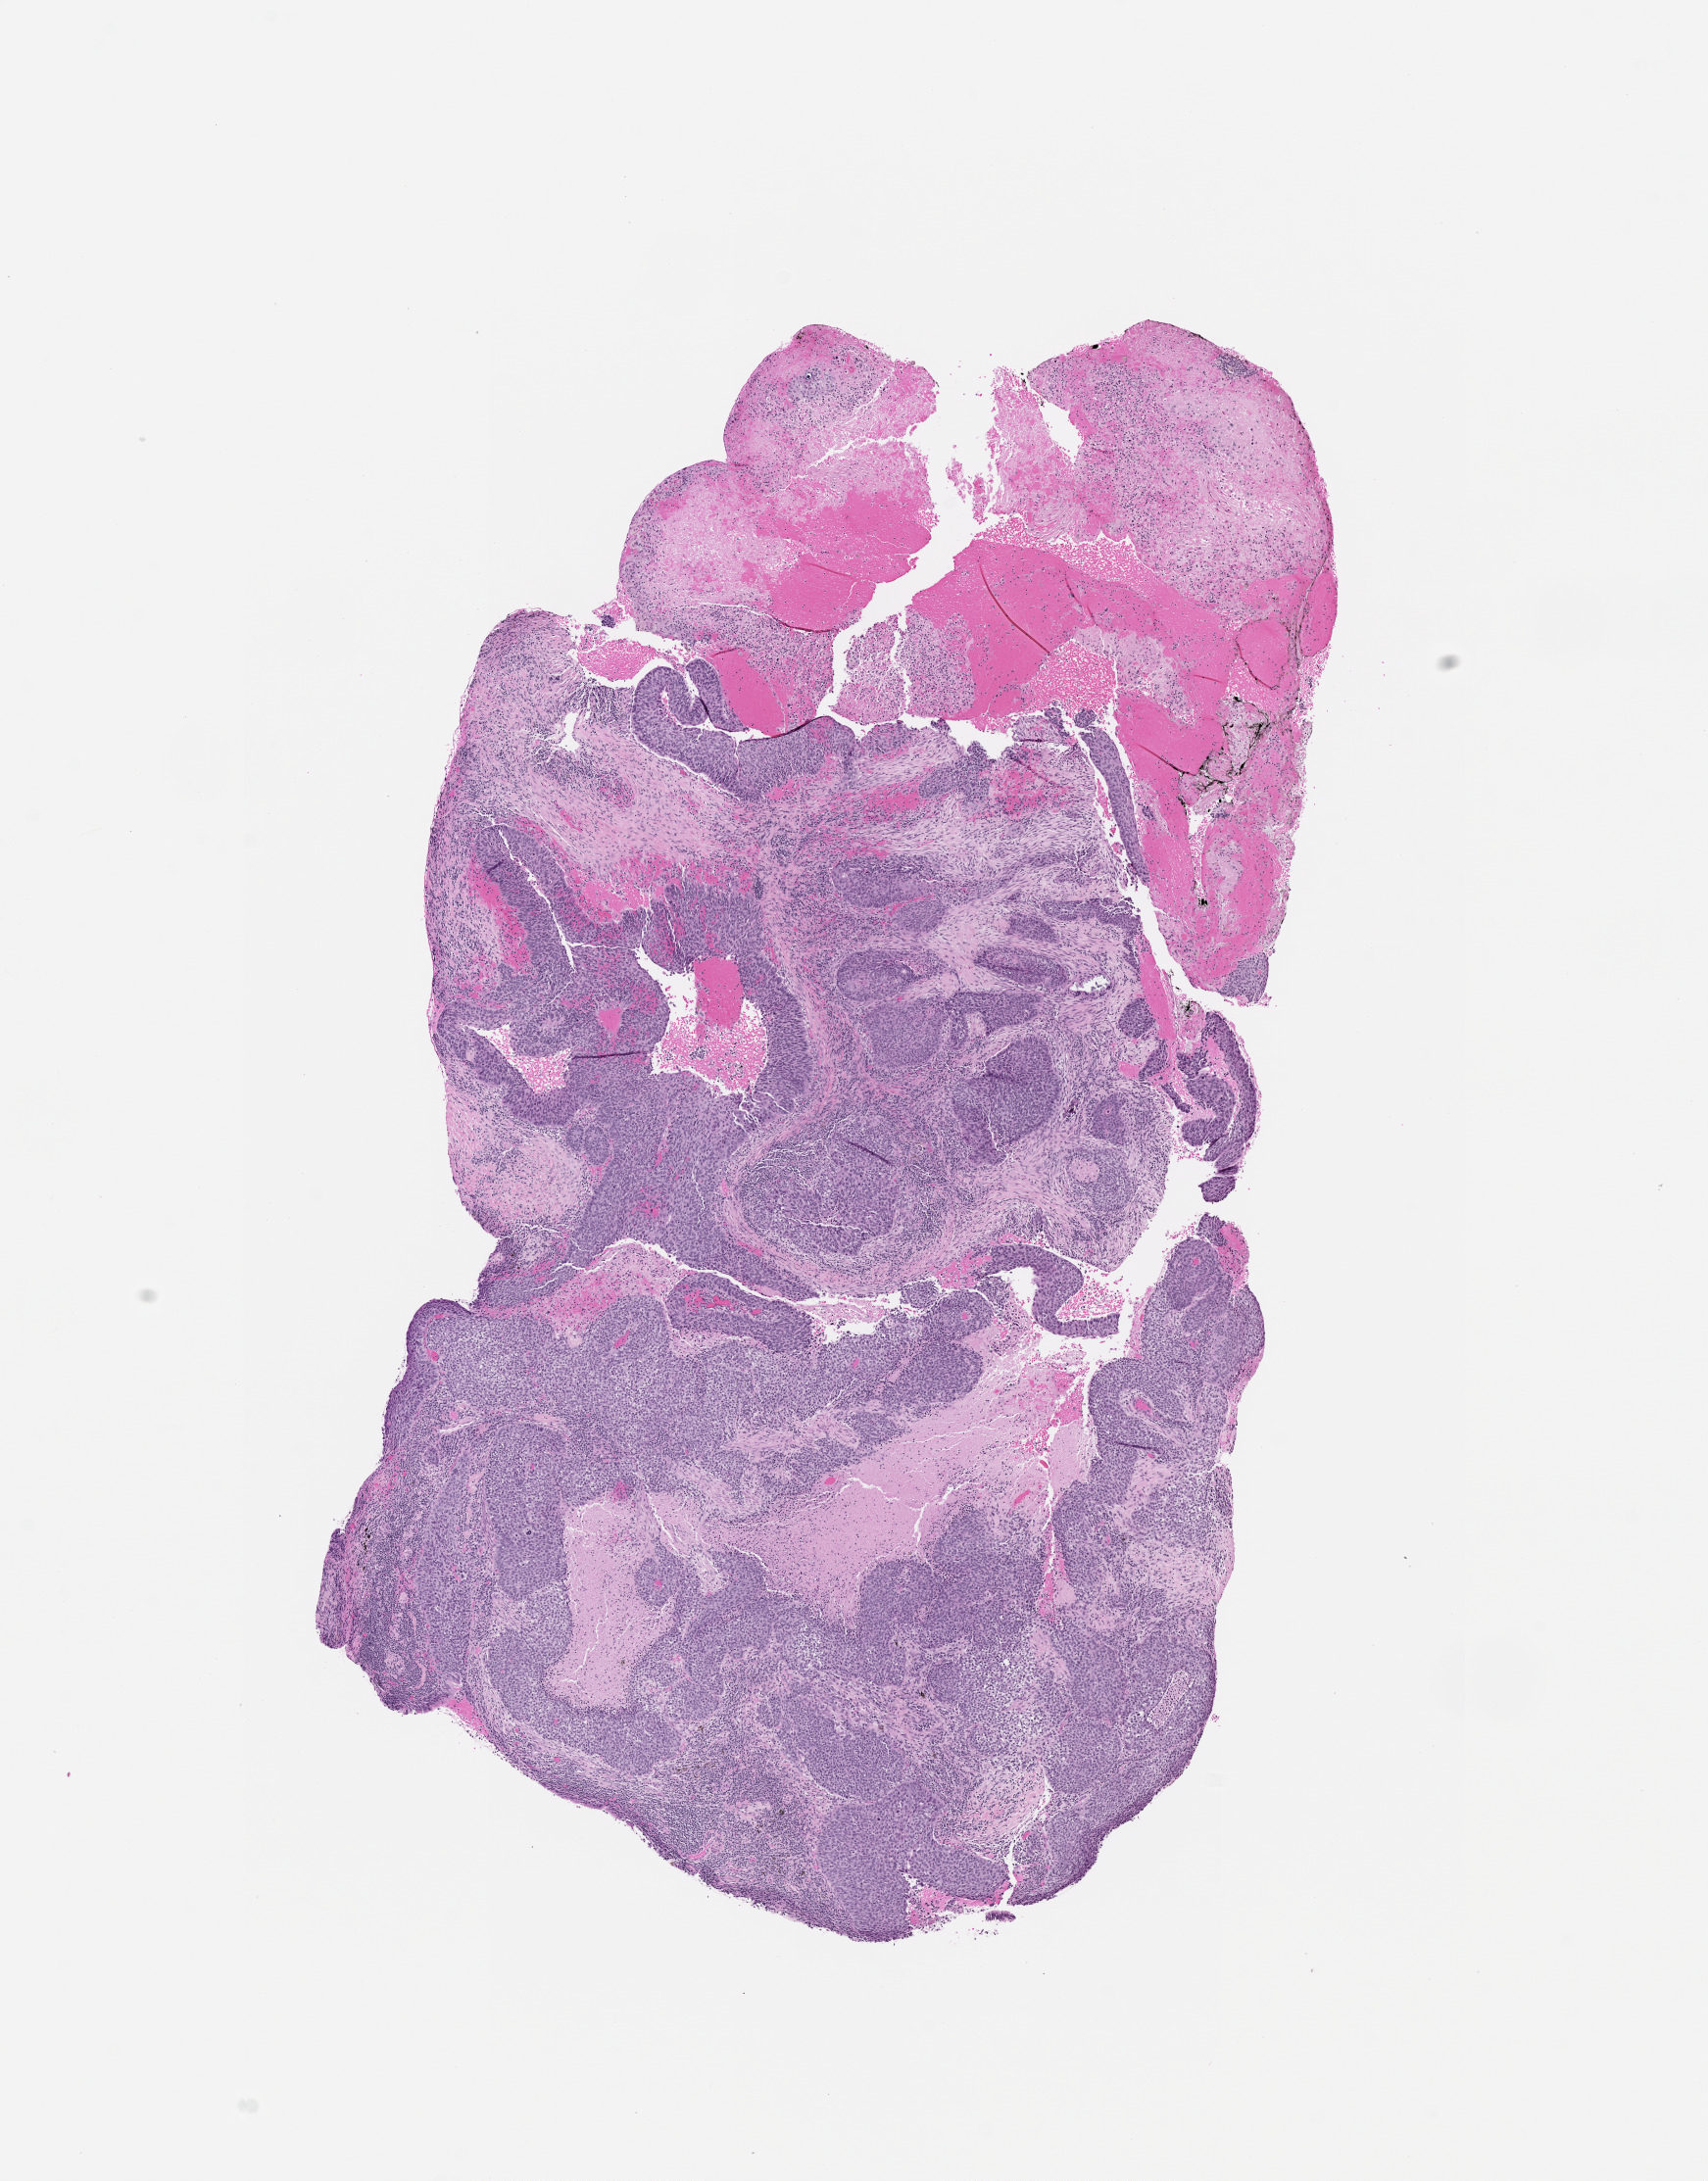
Digitized Hematoxylin and eosin (H&E) stained tissue section (whole slide) — whole scanned area (about 7.0 x 9.0 mm) shown as a low-resolution overview. Tumour tissue sample, lung. Patient: male, age 68 years.
Patient diagnosis (cohort enrolment): squamous cell carcinoma (lung).